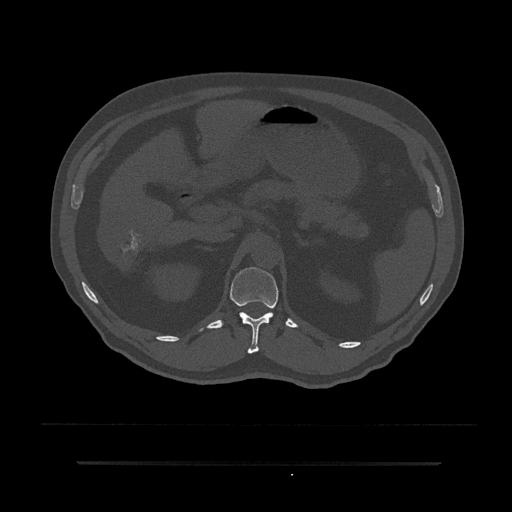
CT including the spine, one axial slice; 120 kVp; bone window (W 1800 / L 400 HU); 0.5 mm slice thickness; 512 × 512 image matrix. Patient: male, 59 years. Case-level facts recorded for this patient, not image findings: primary cancer: bile ducts; vertebrae with lytic lesions (as recorded): T10.
Structures marked on this image (semi-automatically segmented with operator editing):
- T12 vertebra: box from (x=230, y=267) to (x=279, y=354) px